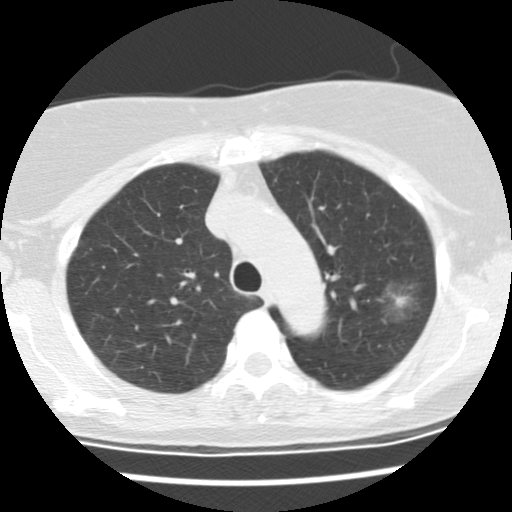
Low-dose screening chest CT, one axial slice; slice 105 of 137 in the series (ordered by position); lung window (W 1500 / L -600 HU); 512 × 512 image matrix, field of view 288 × 288 mm.
Structures marked on this image (expert manual segmentation):
- lesion 1 (tumor, upper lobe of left lung): bounding box <388,293,410,308> (left, top, right, bottom; pixels)